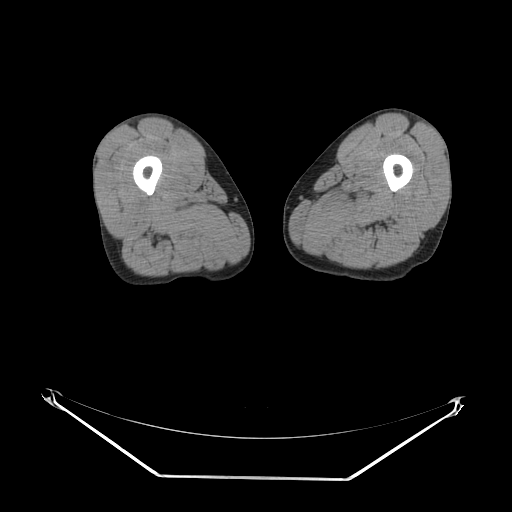
CT of an extremity soft-tissue mass (from a PET/CT study), one axial slice. Slice 5 of 267 in the series (ordered by position). Reconstruction kernel SOFT. 140 kVp. Soft-tissue window (W 400 / L 40 HU). 3.75 mm slice thickness. 512 × 512 image matrix. Male patient. From the clinical record (not read from this slice): histological type: pleiomorphic liposarcoma; grade: high; site of the primary tumour: left thigh.
Annotated regions visible in this slice (expert contour drawn on MRI and transferred to this co-registered scan by the dataset authors):
- gross tumour volume including surrounding oedema: box from (x=336, y=208) to (x=364, y=223) px